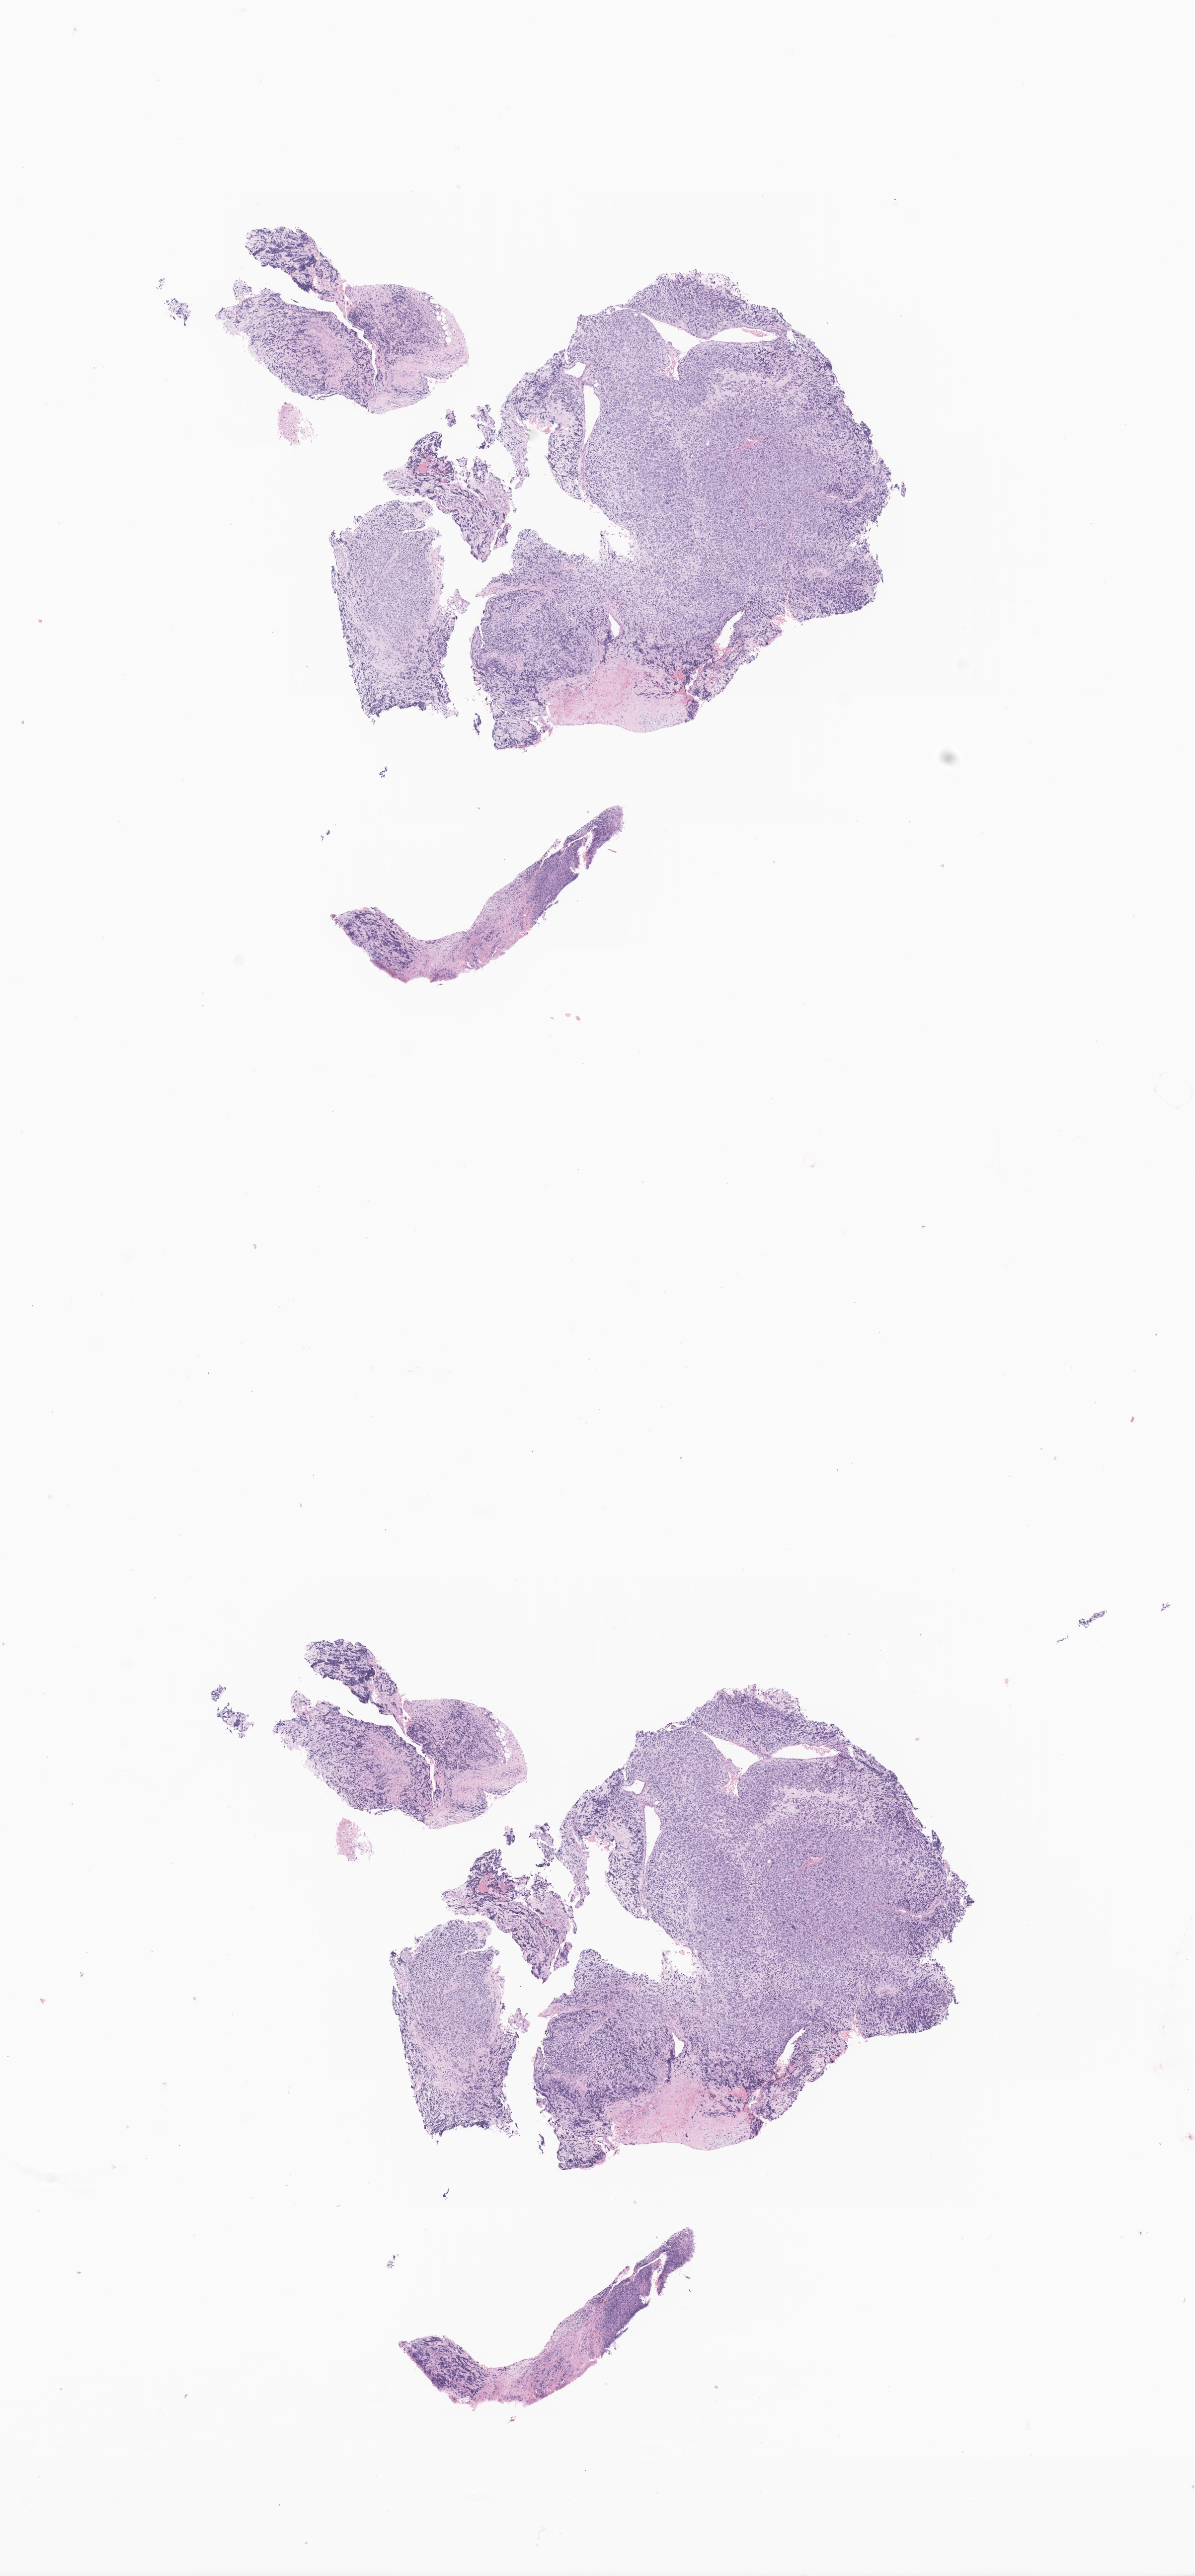
Whole-slide image, hematoxylin and eosin (H&E) stain of tumor tissue from the orbit — a low-resolution overview of the entire scanned area, about 10.1 x 21.9 mm, FFPE section. Patient female; age 118 months (9 years 10 months).
Diagnosis (ICD-O-3 morphology term): Rhabdomyosarcoma, NOS.